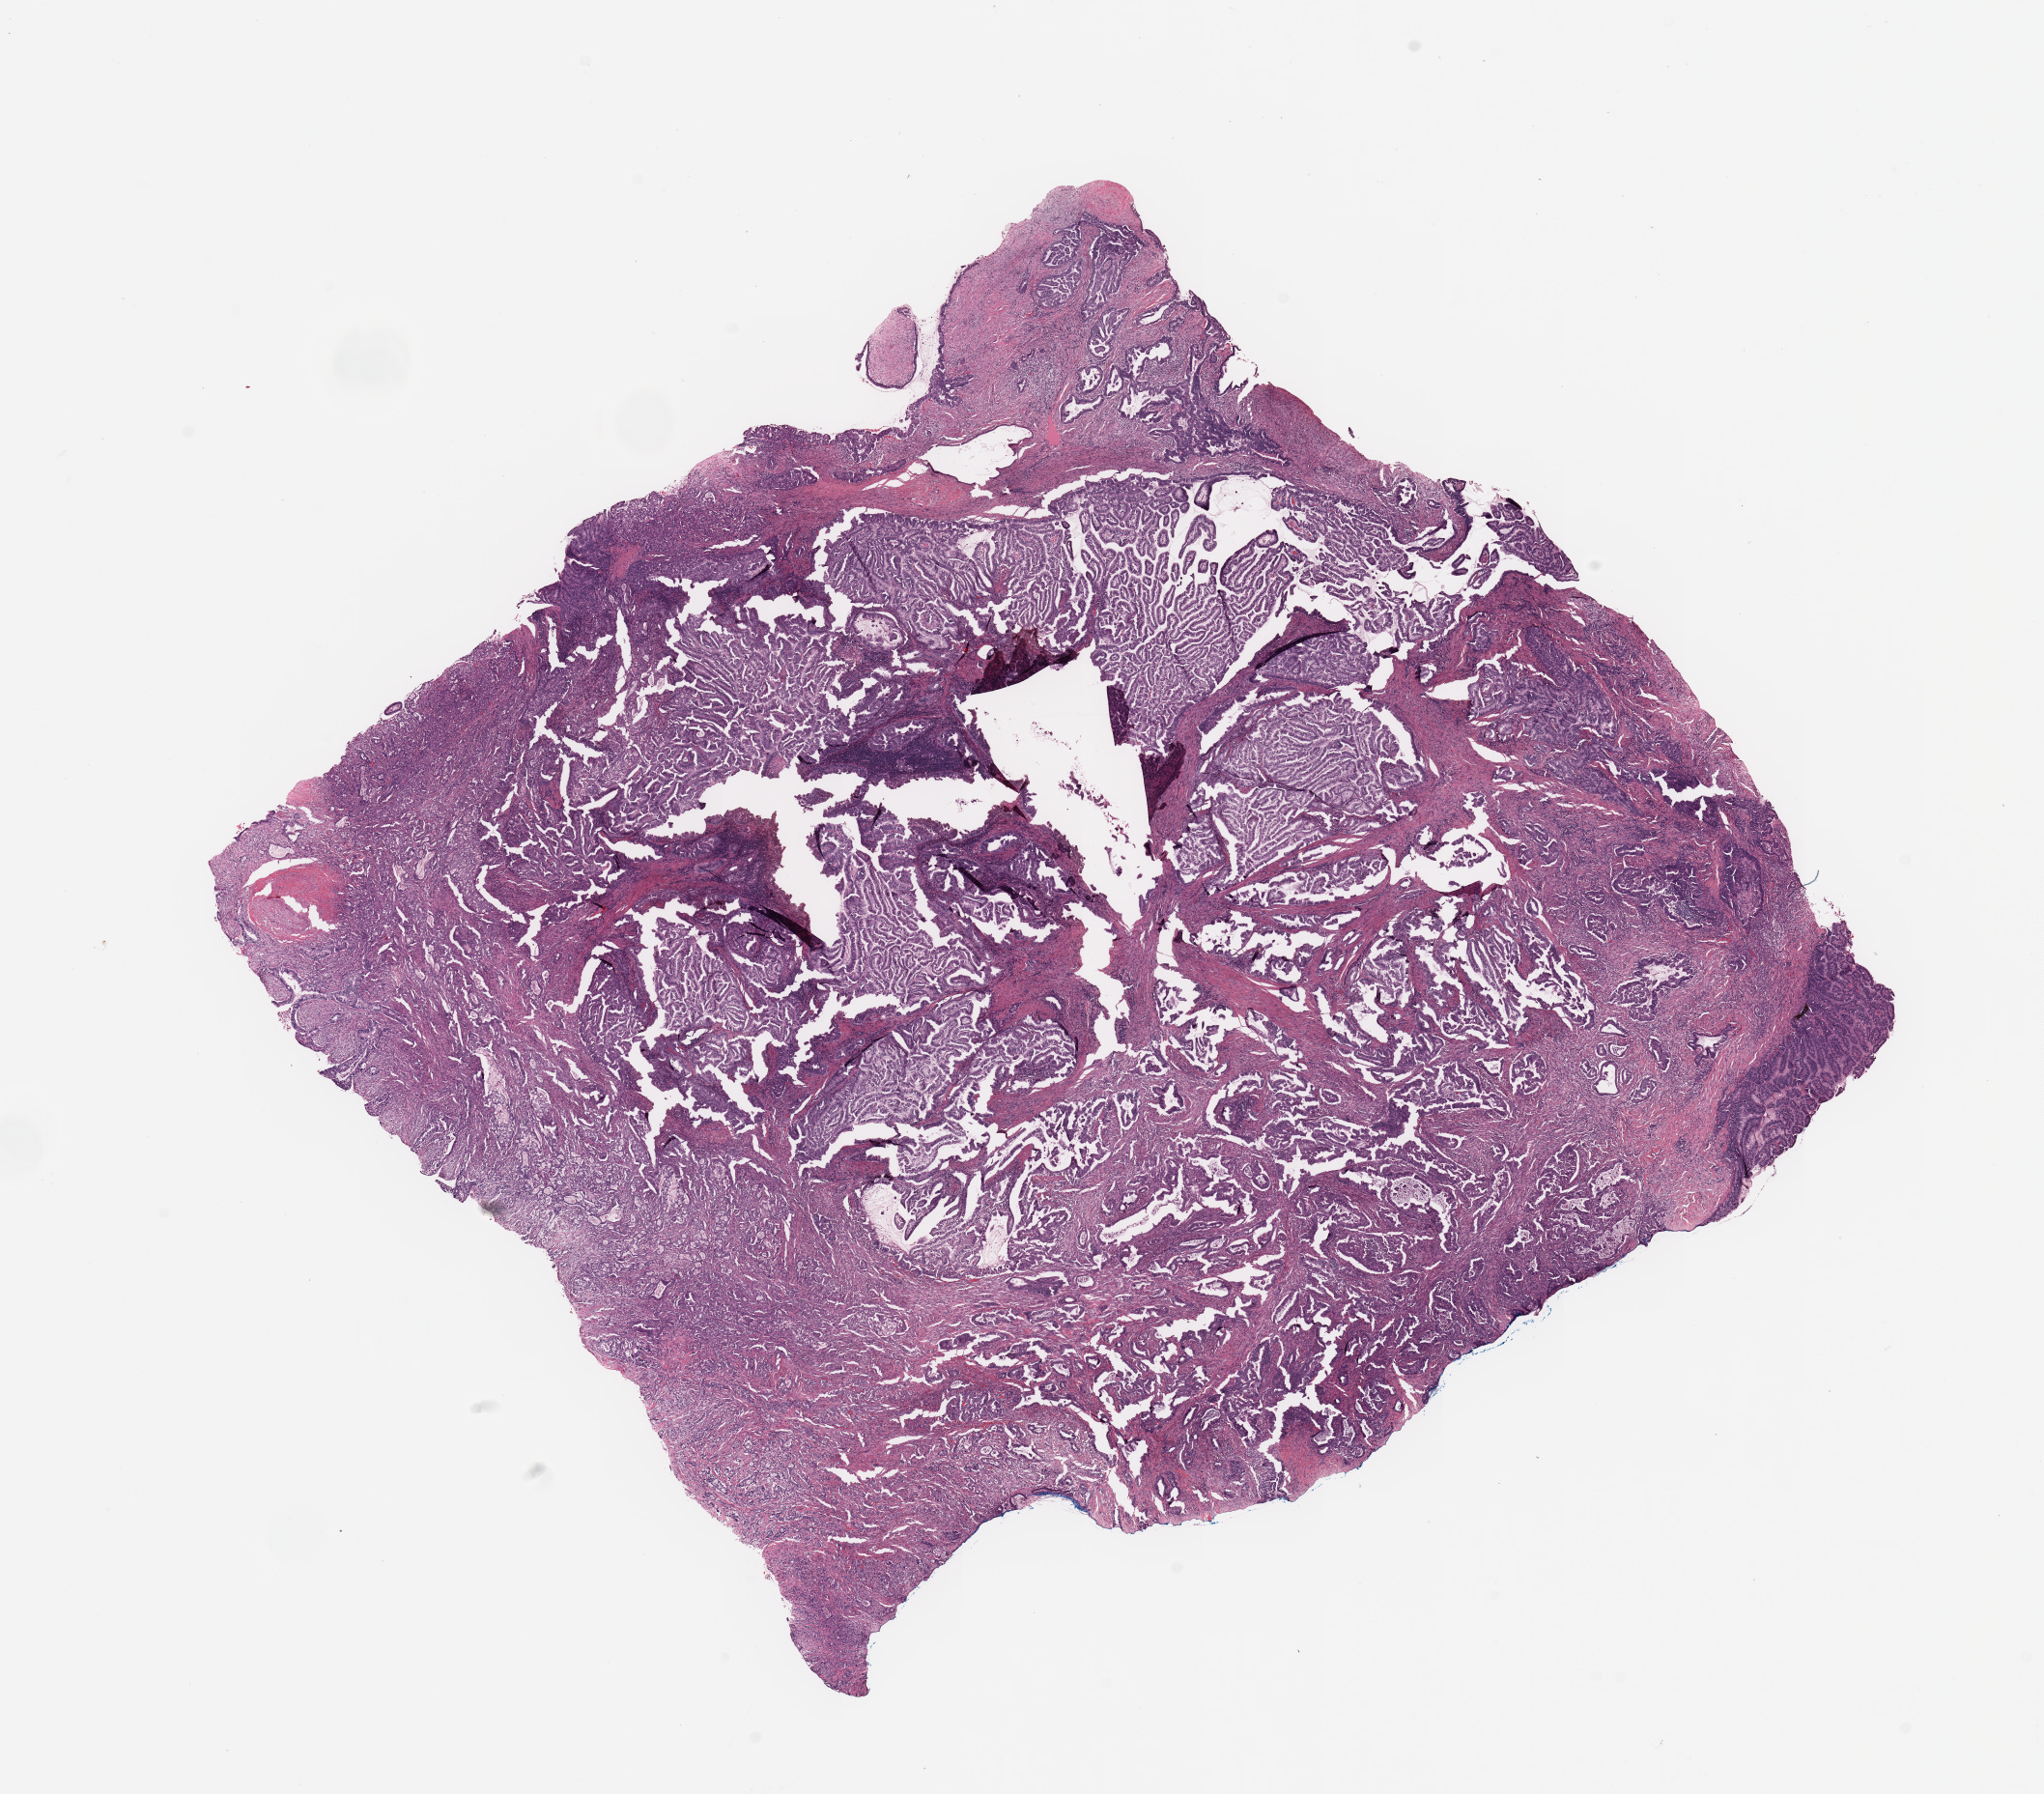
Digitized H&E tissue section (whole slide) — whole scanned area (about 16.7 x 14.7 mm, slide scanned at 20x) shown as a low-resolution overview. Tumour tissue sample, sampled site: pancreas. Patient: male, age 68 years. Histologic grade: G2 (moderately differentiated). Pathologist review of this section (percent, as recorded): tumour nuclei 80%, necrosis 2%.
AJCC pathologic stage: III. Histologic diagnosis: Infiltrating duct carcinoma, NOS. Primary tumour site (as recorded): head.